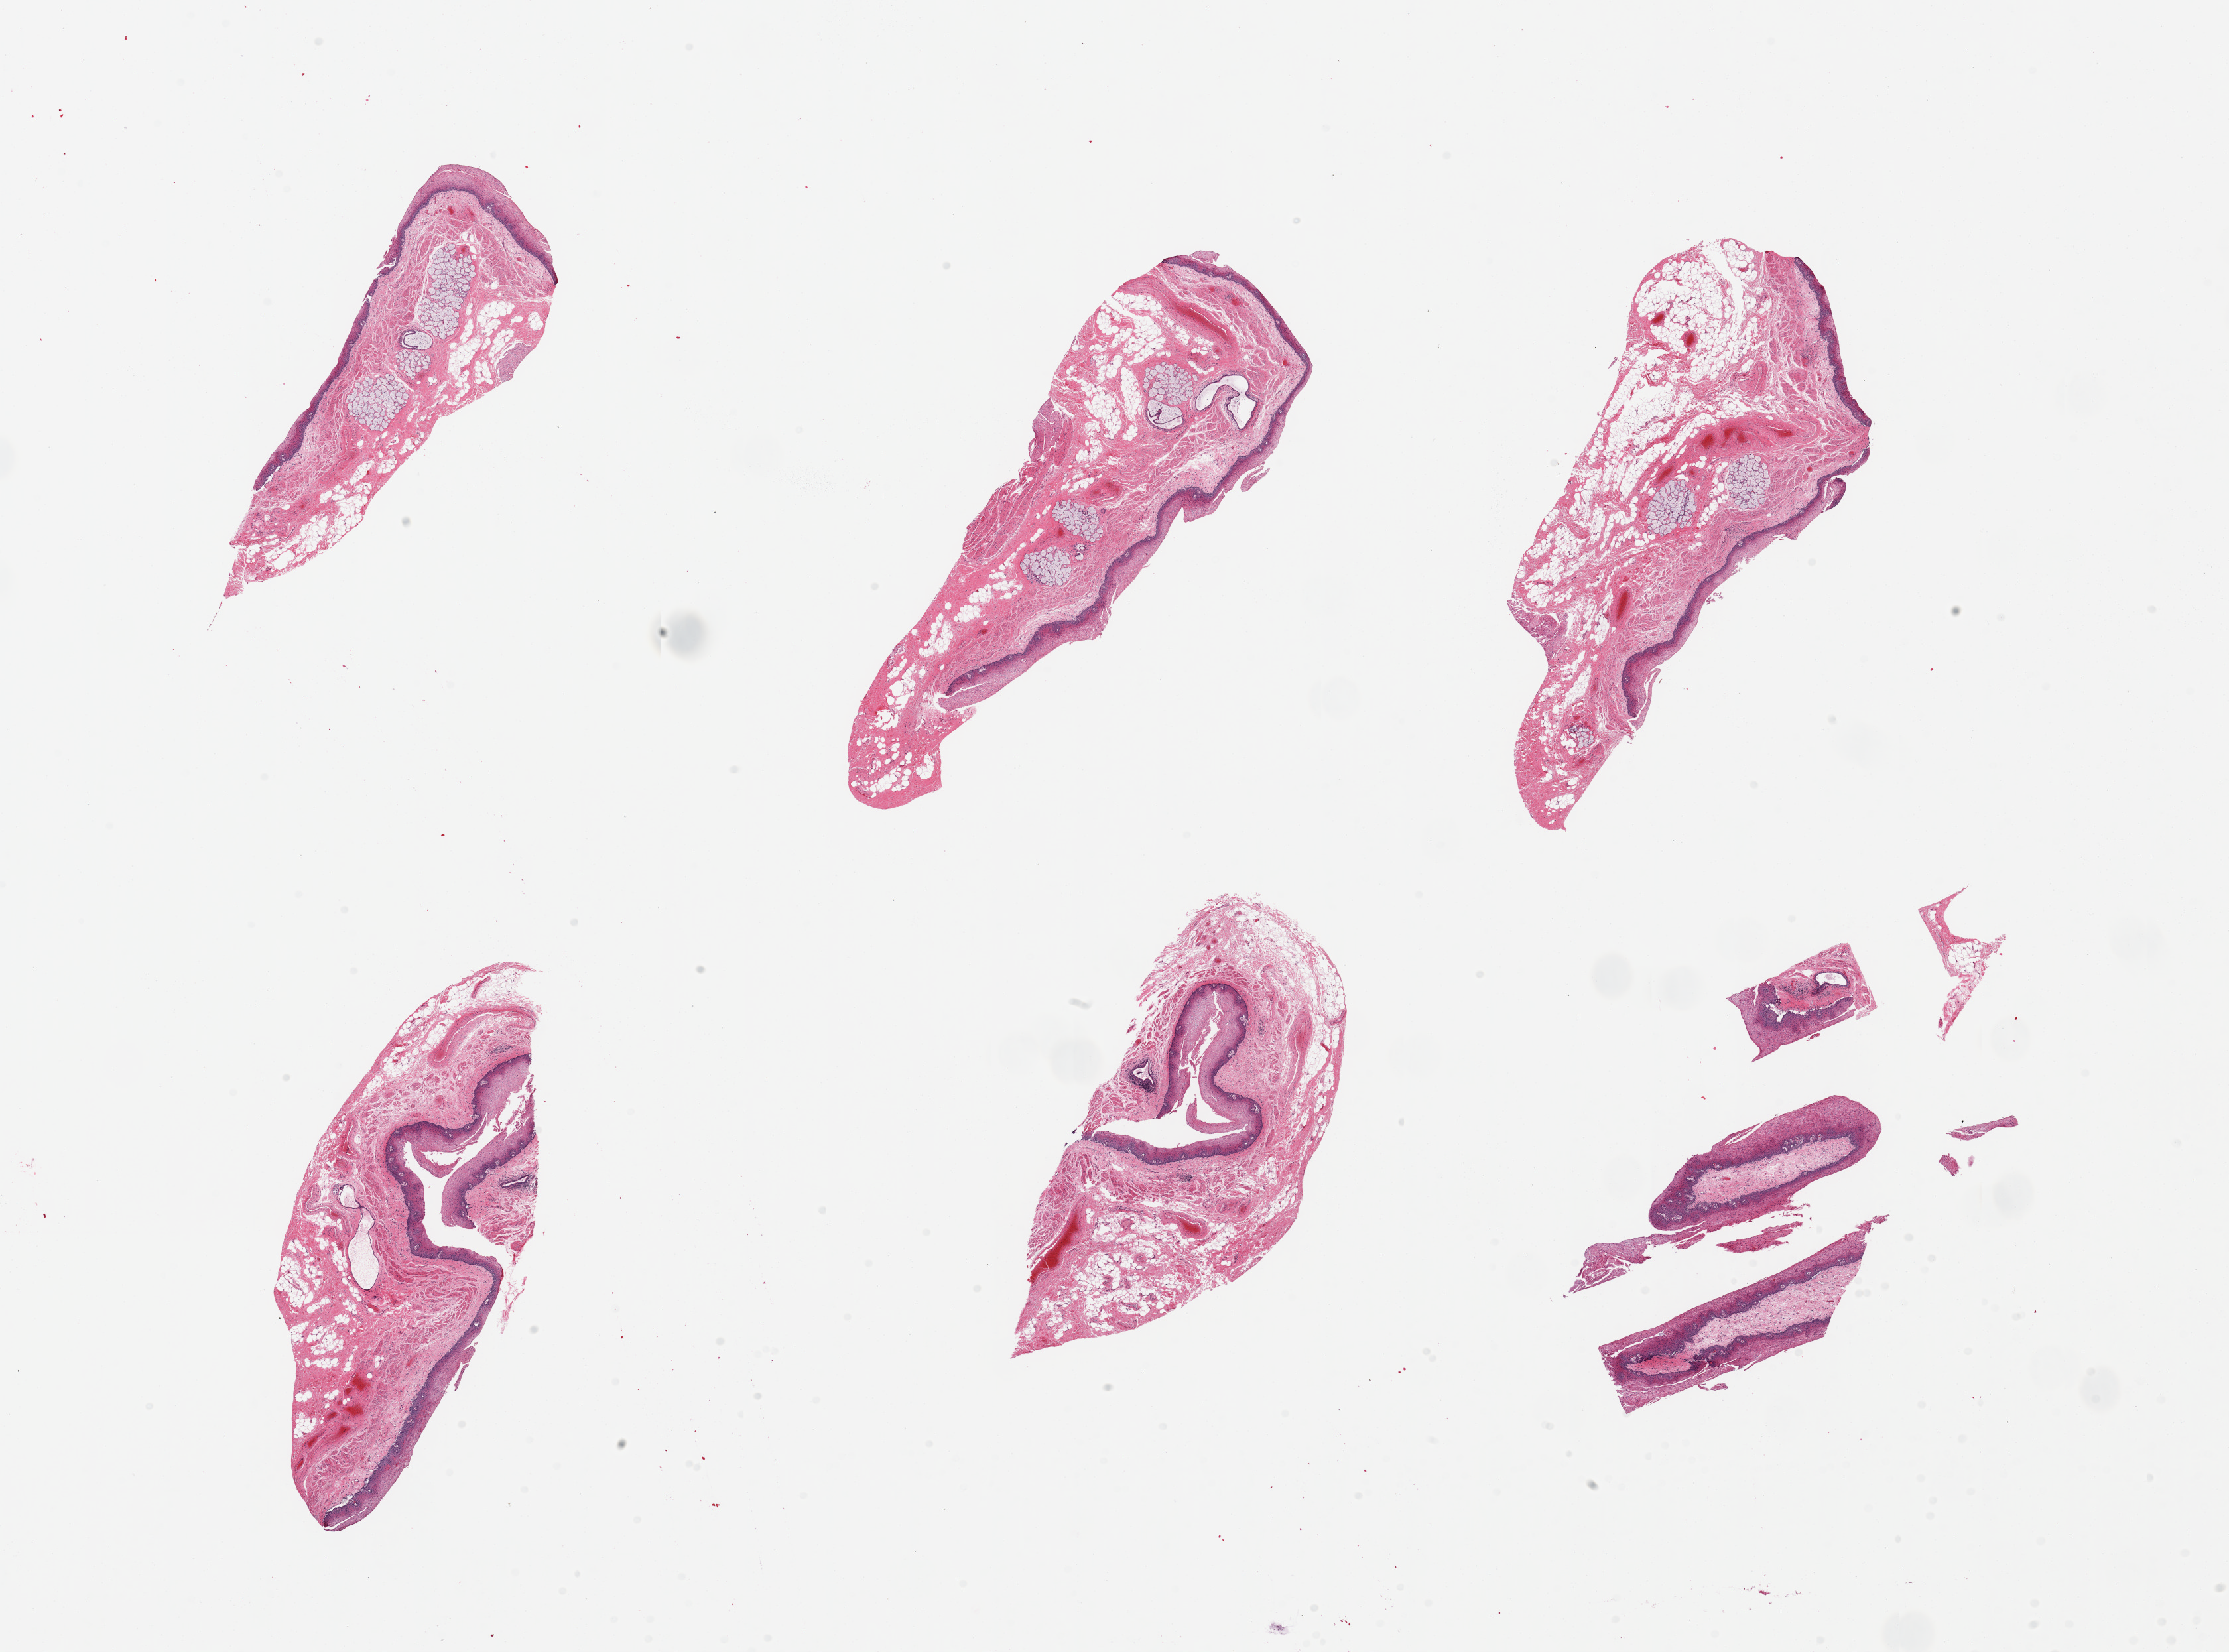
Hematoxylin and eosin (H&E) whole-slide image, brightfield — a low-resolution overview of the entire scanned area, about 26.6 x 19.7 mm (slide scanned at 20x); PAXgene-fixed paraffin-embedded (PFPE) section; sampled site (target tissue): esophageal mucous membrane; donor tissue sample. Donor: male.
• pathologist's review note for this sample: 6 pieces, squamous mucosa partially sloughing, up to~0.3mm, ~10-15% thickness; submucosal mucus glands present